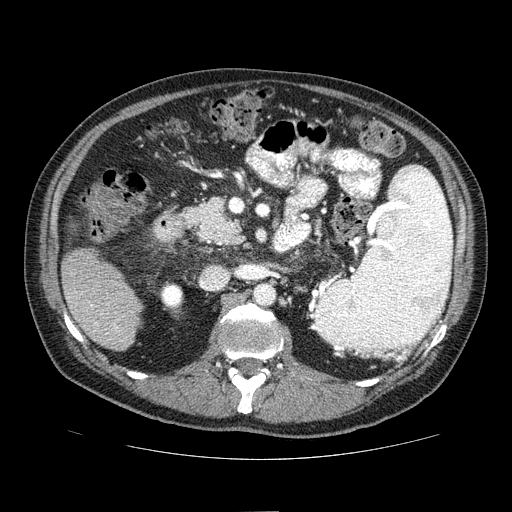
Contrast-enhanced abdominal CT (liver protocol), one axial slice; slice 25 of 81 in the series (ordered by position); one of 2 acquisitions stored at this slice position; soft-tissue window (W 400 / L 40 HU); 2.5 mm slice thickness; 512 × 512 image matrix. Case-level facts recorded for this patient, not image findings: diagnosis: hepatocellular carcinoma (patient treated with transarterial chemoembolisation; whether this scan precedes or follows treatment is not stated here); TNM stage (as recorded): Stage-IIIA; Child-Pugh class: A; tumour nodularity: multinodular.
Outlined on this slice (semi-automatically segmented with operator editing):
- liver parenchyma outside the tumour (the mass and vessels are separate outlines, so this box may not span the whole liver): bounding box <60,248,142,350> (left, top, right, bottom; pixels)
- liver vessels: <91,304,118,330>